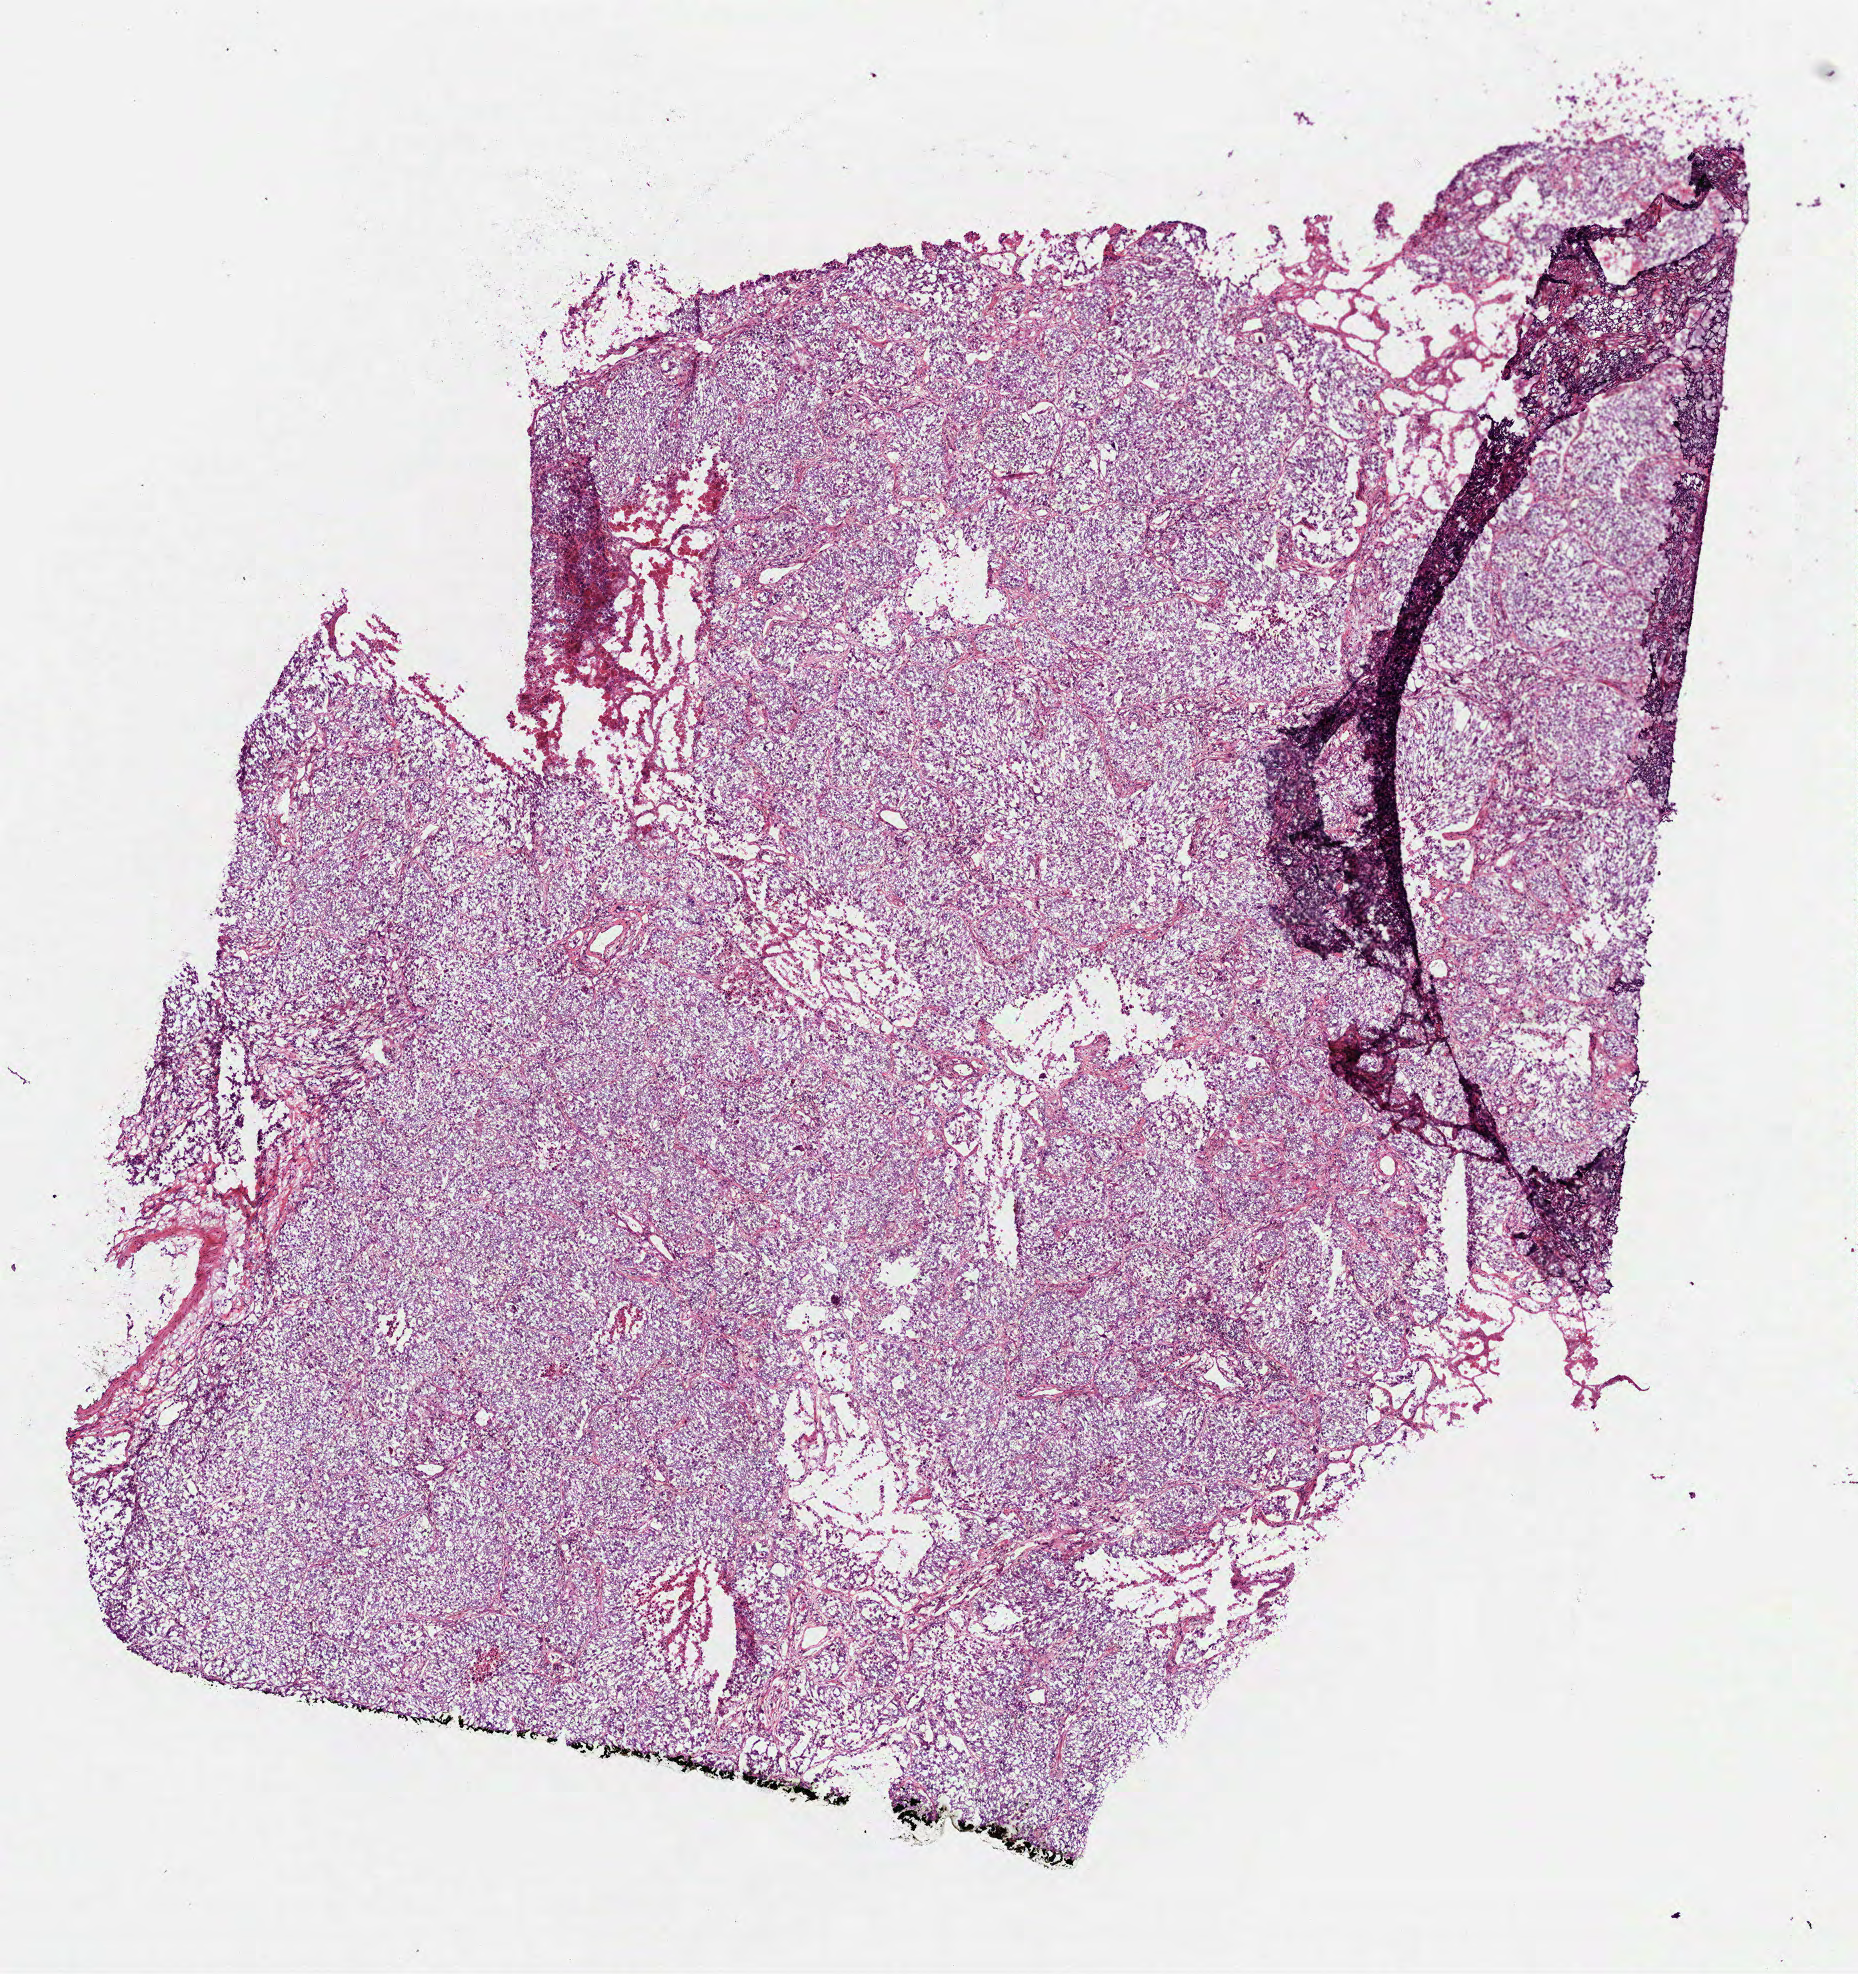
Whole-slide histology image, Hematoxylin and eosin (H&E) stained — whole scanned area (about 7.5 x 8.0 mm, slide scanned at 40x) shown as a low-resolution overview; frozen section from the bottom of the tissue portion; primary tumour sample from the lung. Patient: female, age at initial diagnosis 71 years. Composition of this section per pathologist review: tumour cells 77%, tumour nuclei 80%, normal cells 0%, stromal cells 5%, necrosis 18%.
AJCC pathologic stage: IIIA (6th edition). Diagnosis: Adenocarcinoma with mixed subtypes (lower lobe, lung).